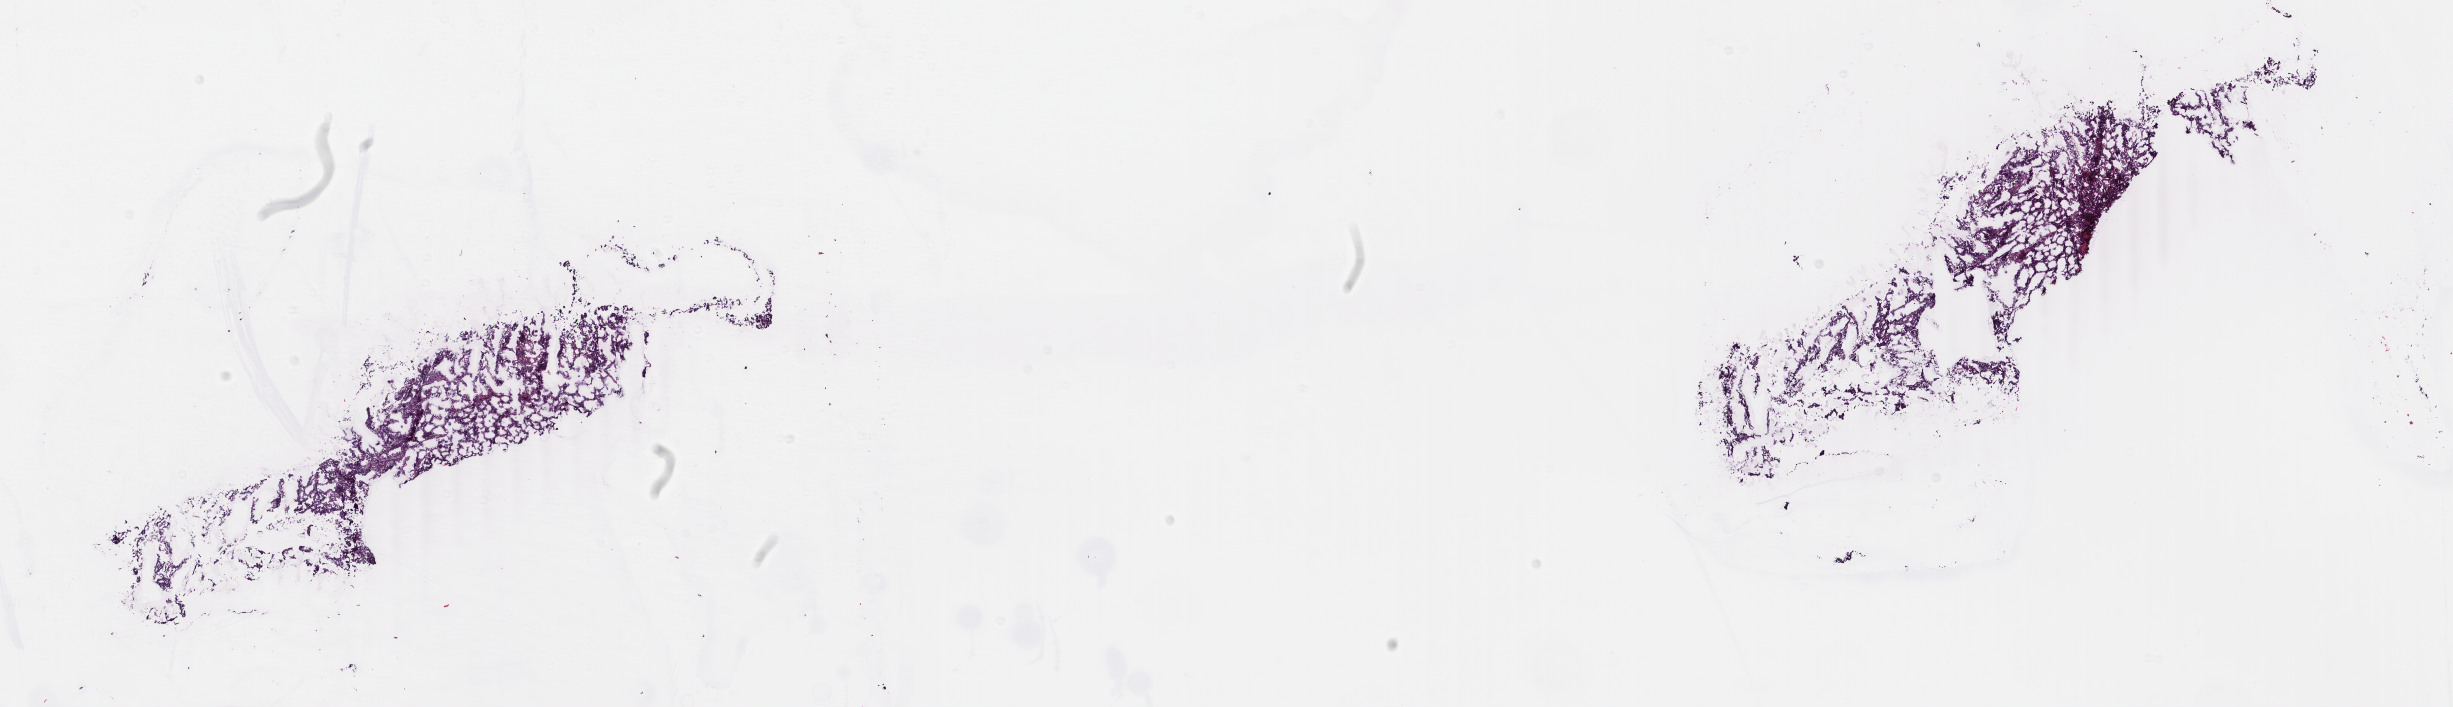
Digitized H&E-stained tissue section (whole slide) — shown as a low-resolution overview of the whole scanned area (about 19.5 x 5.6 mm, acquisition: 40x scan). Frozen section from the bottom of the tissue portion. Uterus, primary tumour sample. Female patient; age at initial diagnosis 37 years. Histologic grade: G2 (moderately differentiated). Composition of this section per pathologist review: tumour cells 80%, tumour nuclei 80%, normal cells 0%, stromal cells 10%, necrosis 10%. Infiltration values recorded for this section: lymphocyte infiltration 5%, monocyte infiltration 0%, neutrophil infiltration 0%.
FIGO stage: IIIA. Pathologic diagnosis: Endometrioid adenocarcinoma, NOS (endometrium).